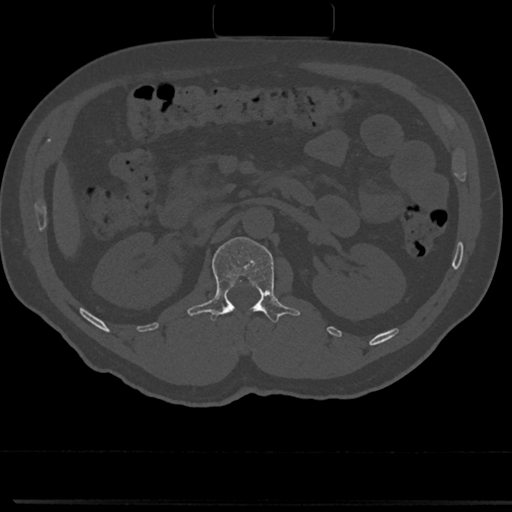
CT including the spine, one axial slice. Position 84 of 817 along the scan axis. Reconstruction kernel Br40s/3. 120 kVp. Bone window (W 1800 / L 400 HU). 0.5 mm slice thickness. 512 × 512 image matrix. Male patient, age 61 years. Case-level facts recorded for this patient, not image findings: primary cancer: prostate.
Structures marked on this image (semi-automatically segmented with operator editing):
- L1 vertebra: bounding box <191,238,298,324> (left, top, right, bottom; pixels)